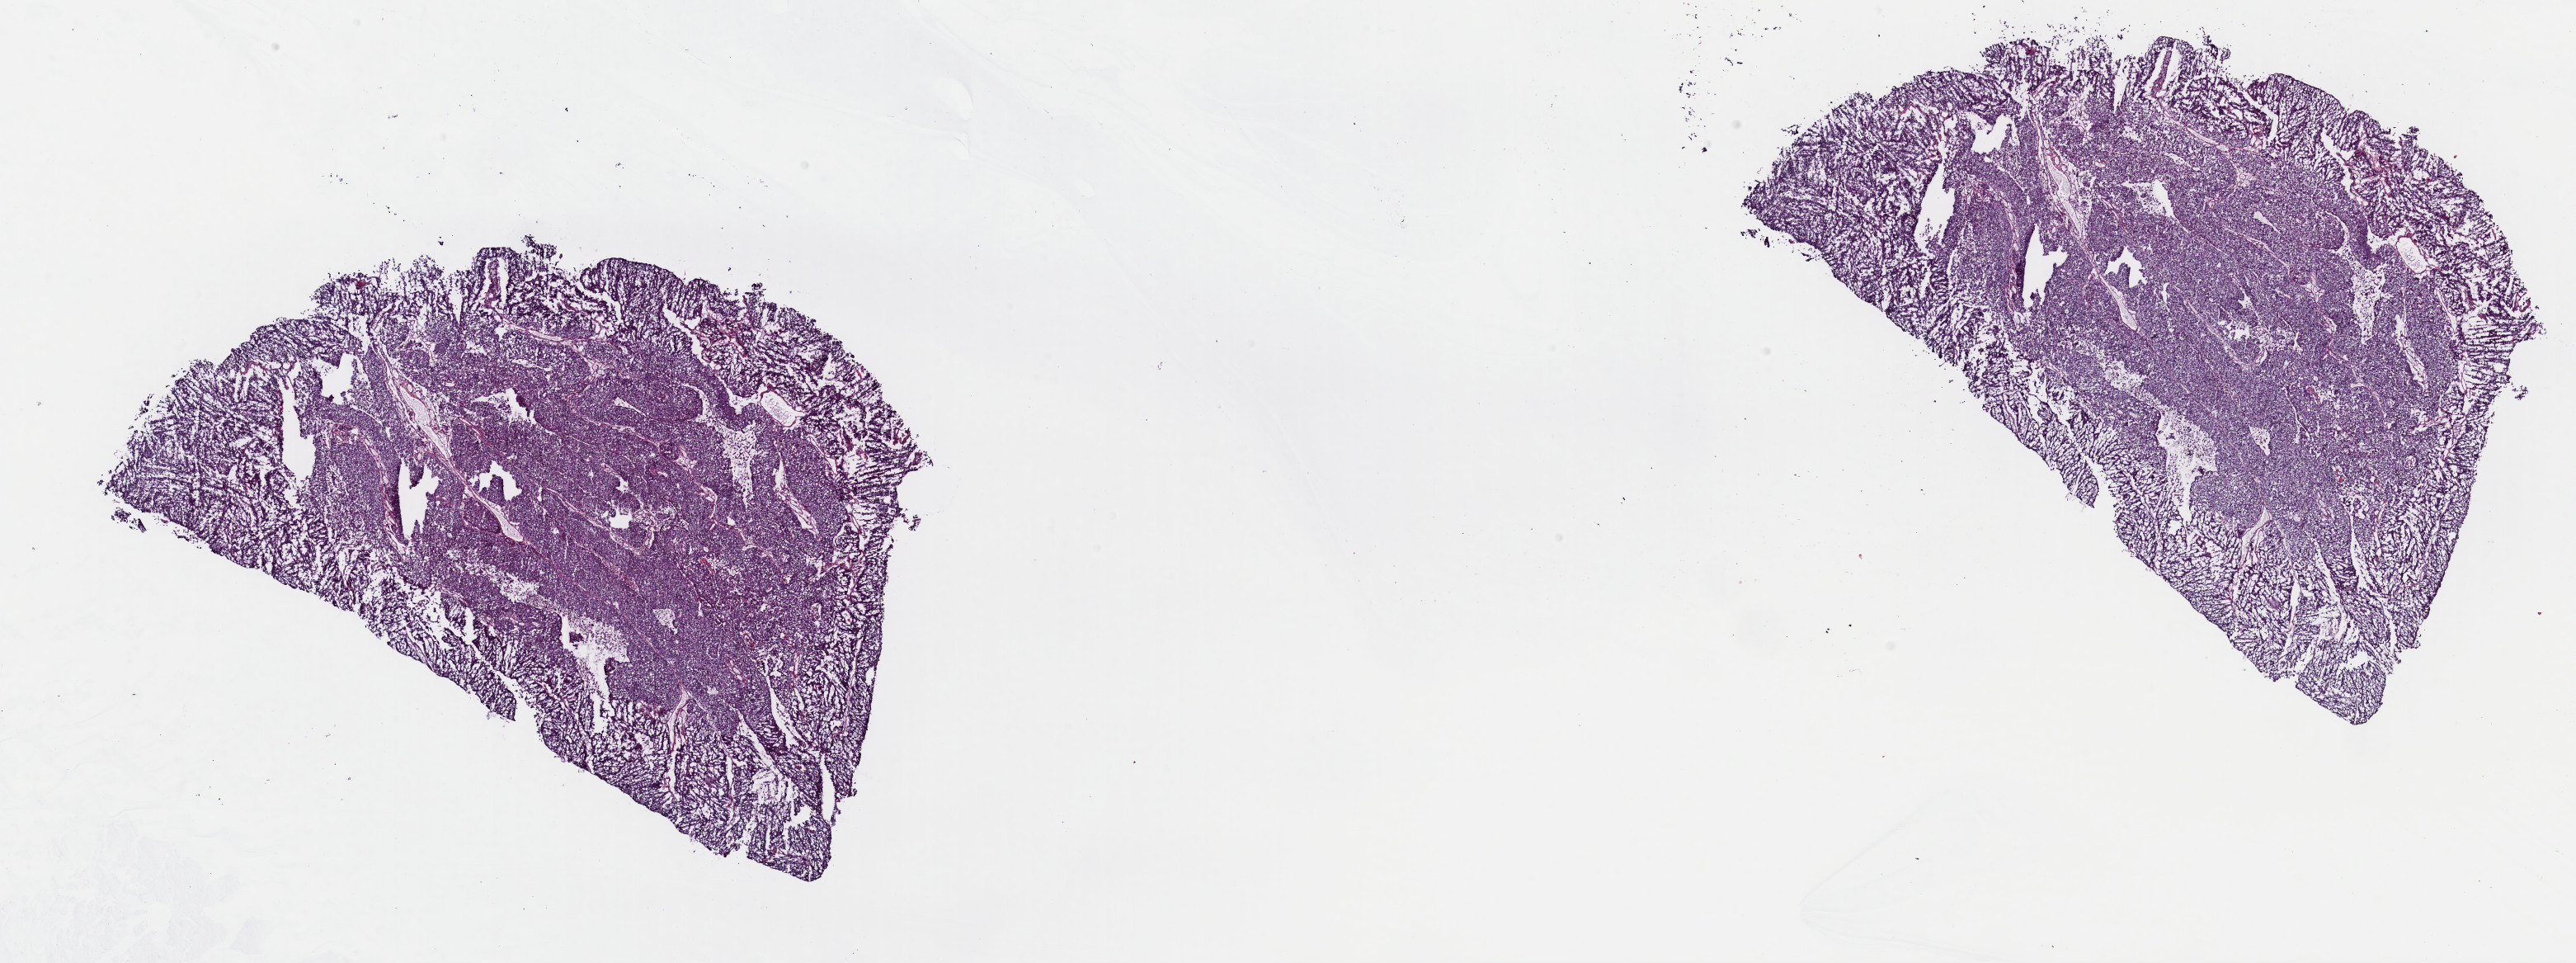
H&E whole-slide image — whole scanned area (about 24.7 x 9.2 mm) shown as a low-resolution overview; frozen section from the top of the tissue portion; primary tumour sample from the bladder. Male patient; age at initial diagnosis 58 years. Histologic grade: high grade. Pathologist review of this section (percent, as recorded): tumour cells 96%, tumour nuclei 99%, normal cells 0%, stromal cells 1%, necrosis 3%. Infiltration values recorded for this section: lymphocyte infiltration 0%, monocyte infiltration 0%, neutrophil infiltration 0%.
AJCC pathologic stage: IV (7th edition). Histologic diagnosis: Transitional cell carcinoma. Lymph nodes positive (case pathology): 1 of 54 examined.